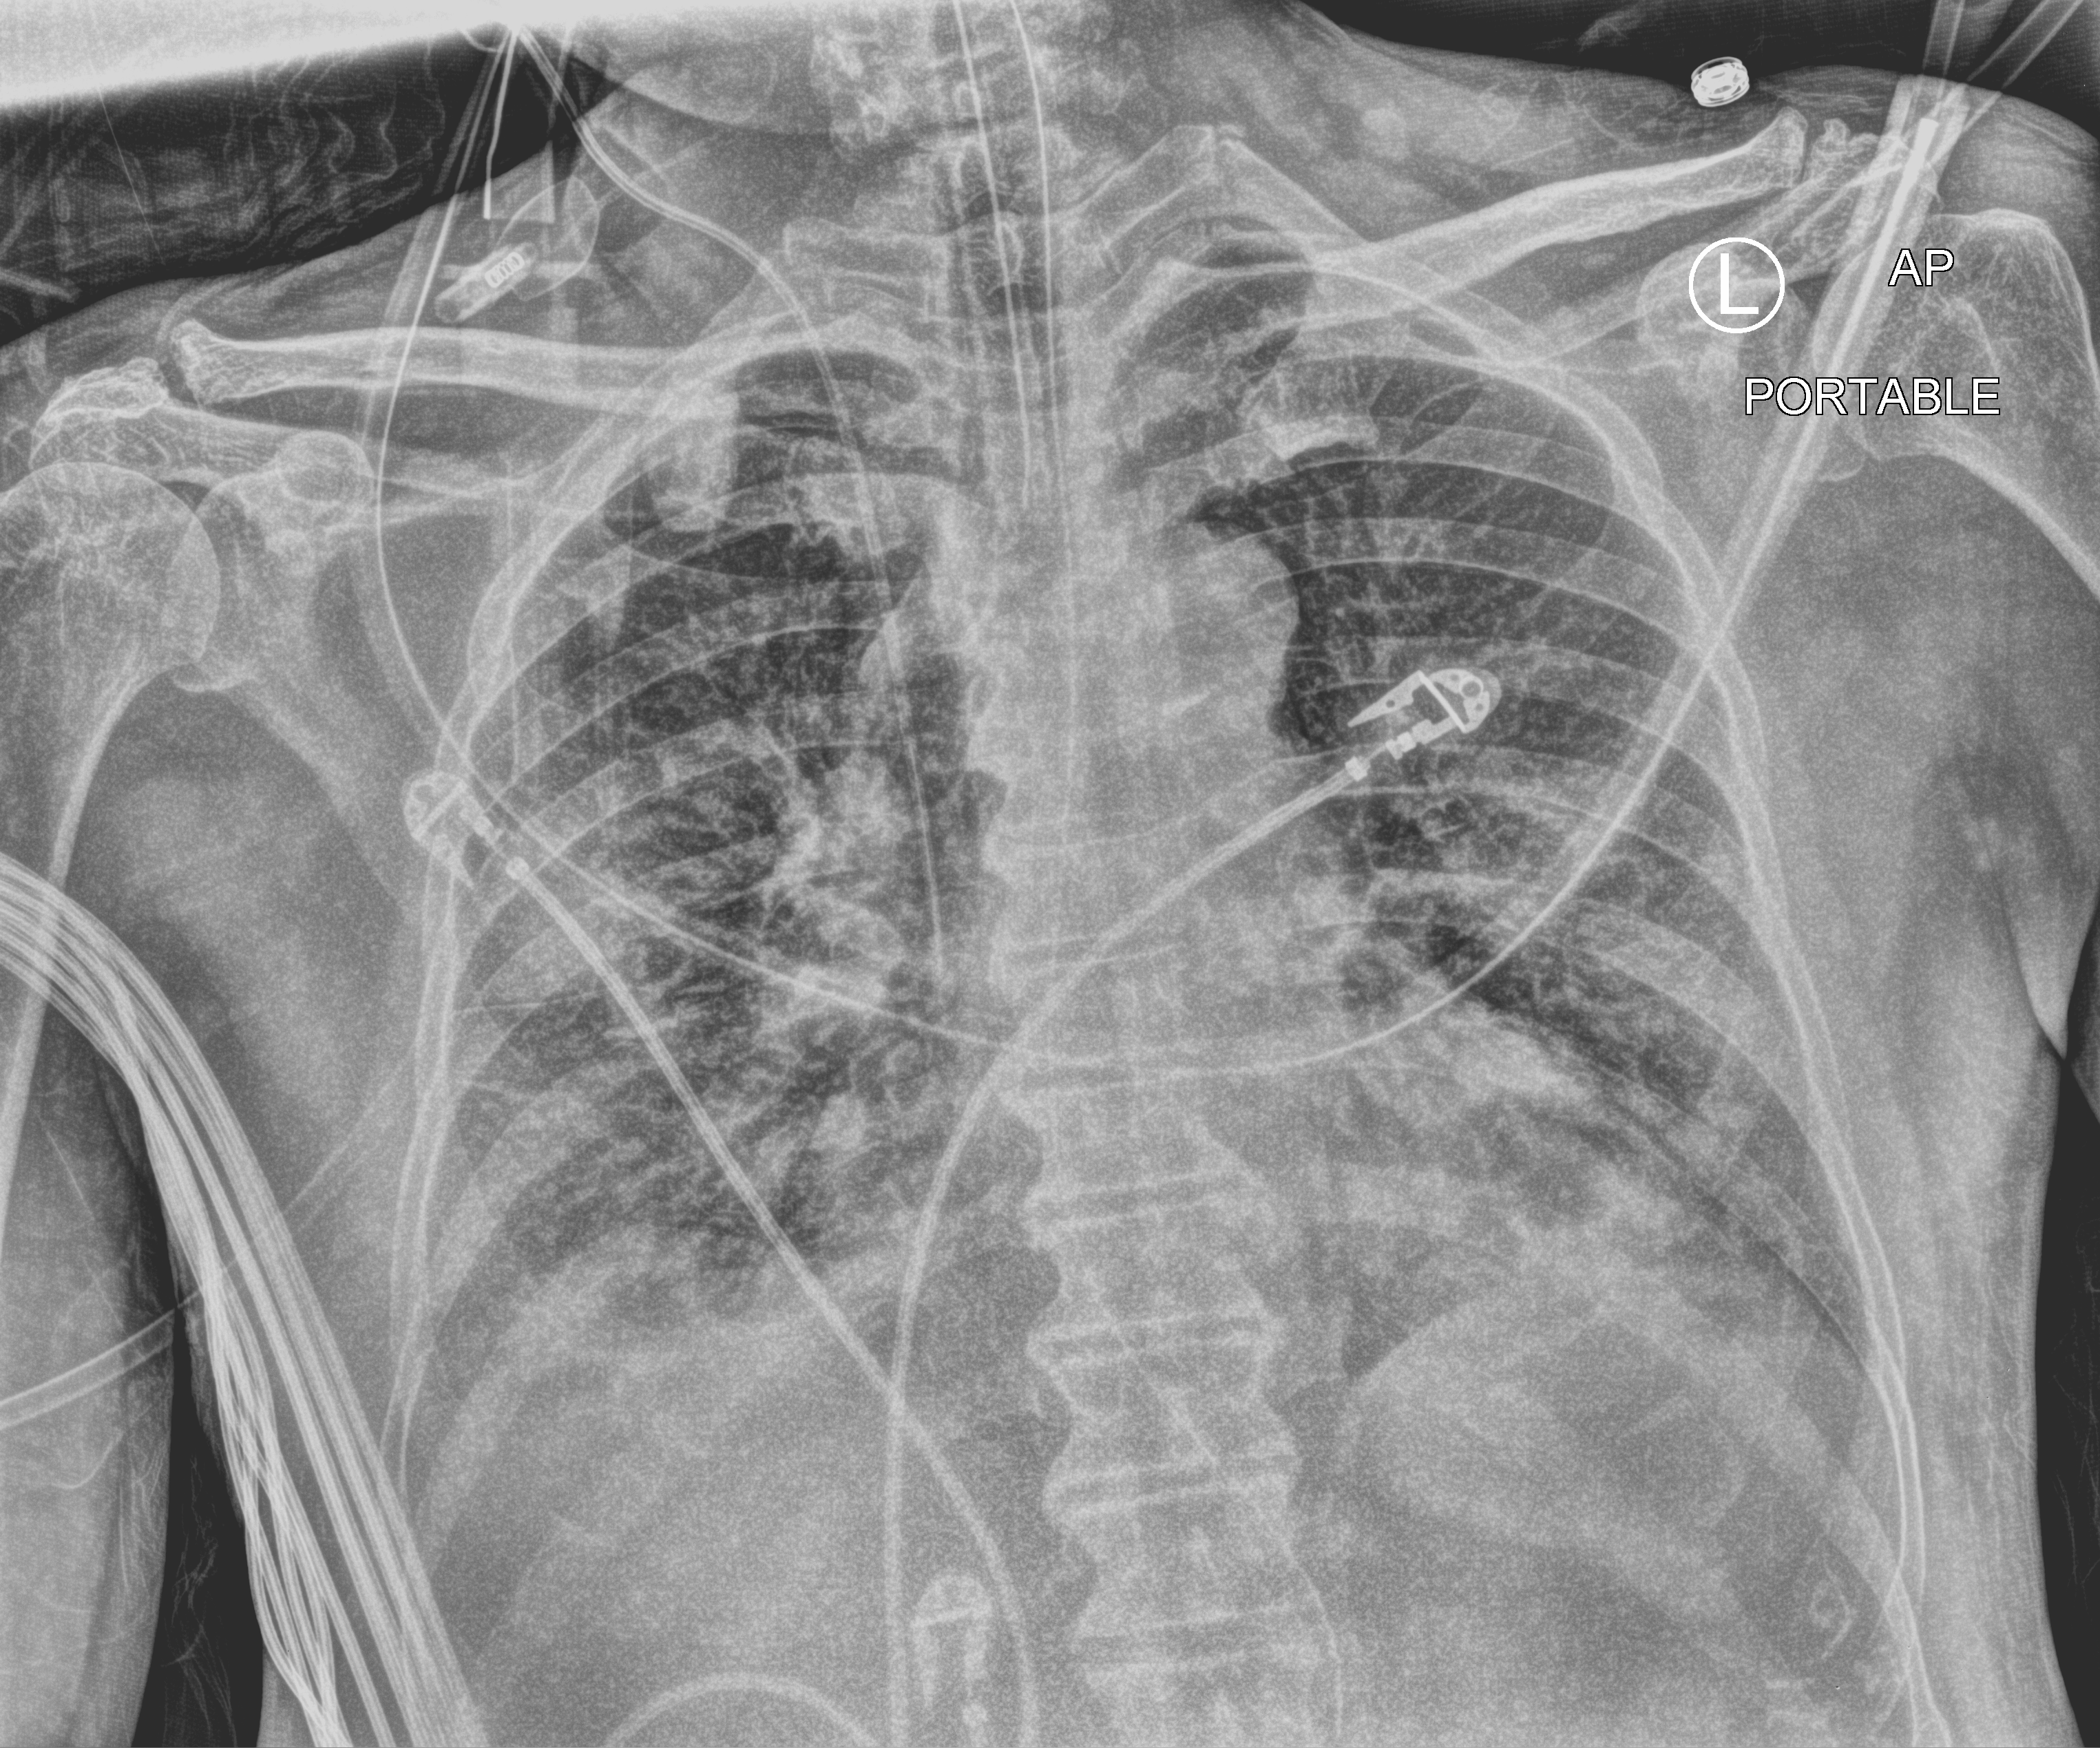
Chest X-ray (portable). Patient hospitalised with COVID-19; male, aged 60–74 years.
From the hospital-stay record, not from the radiograph (when in the stay this image was taken is not recorded):
- length of hospital stay: 26 days
- admitted to intensive care during this hospital stay: yes
- mechanically ventilated during this hospital stay: yes